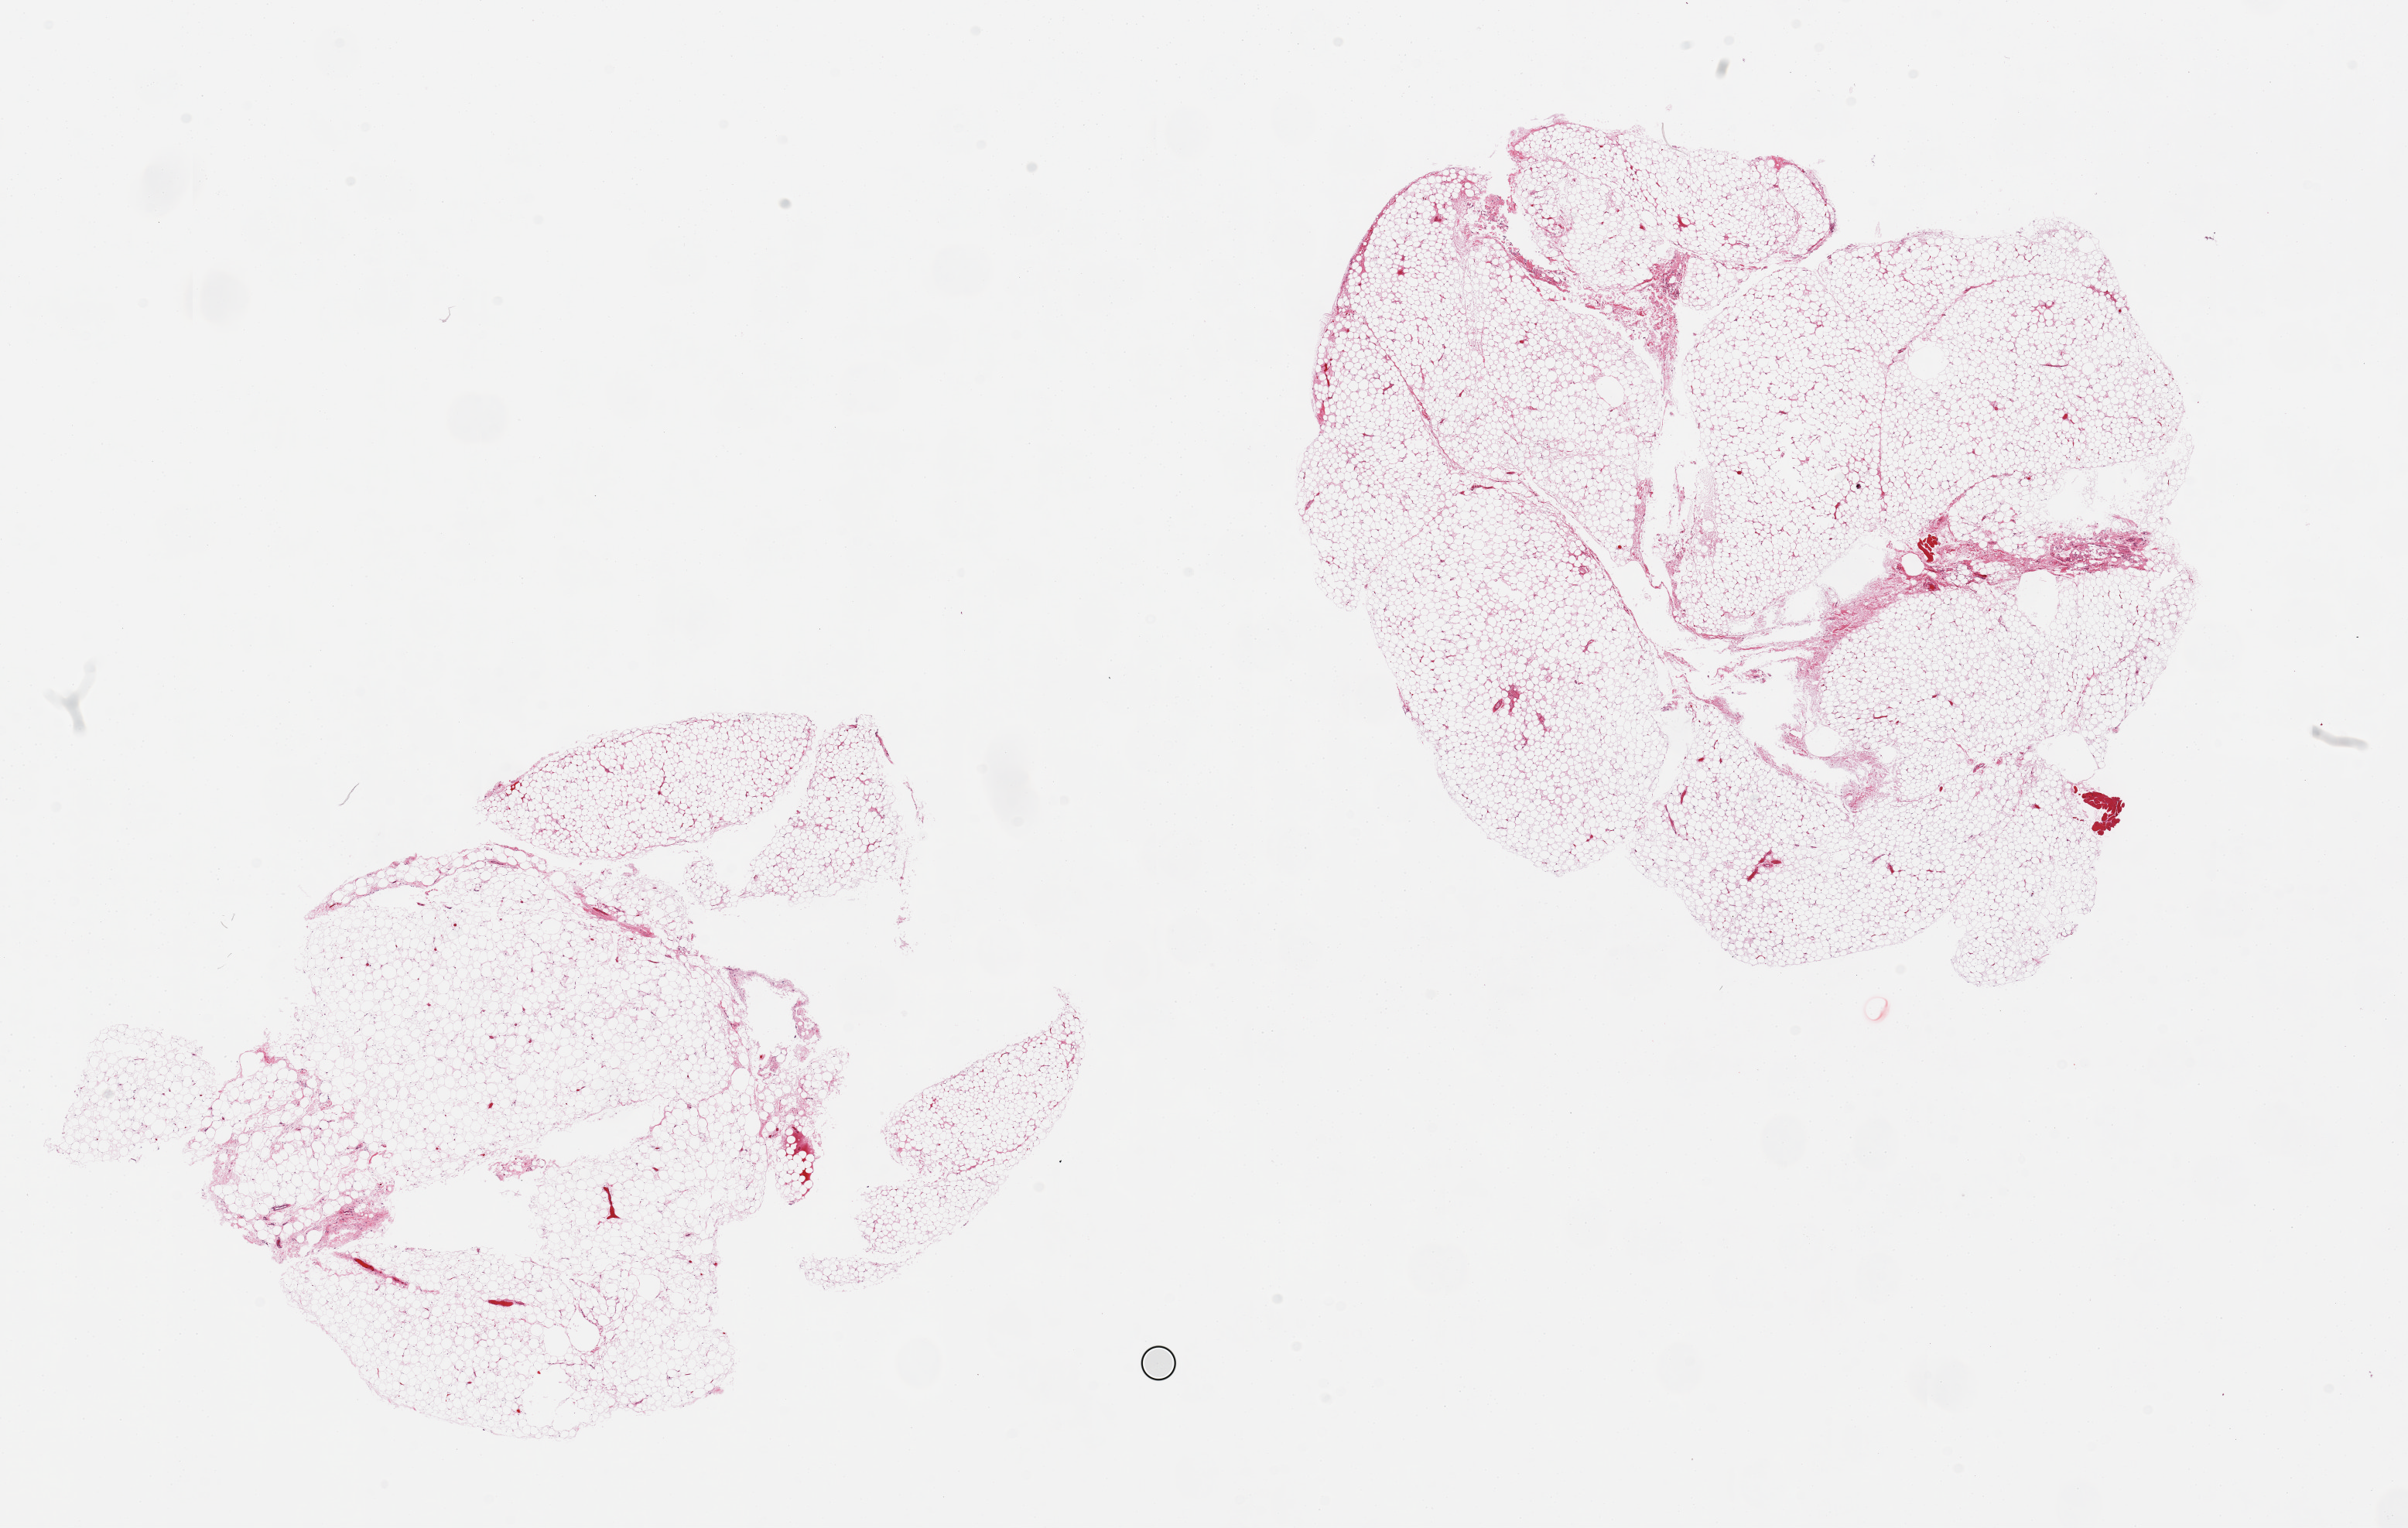
Digitized haematoxylin and eosin-stained section, a low-resolution overview of the entire scanned area, about 24.6 x 15.6 mm (slide scanned at 20x); PAXgene-fixed, paraffin-embedded tissue; sampled site (target tissue): adrenal gland; tissue donor sample.
Review note (as recorded): 2 pieces, adipose tissue, not adrenal, few foci of skeletal muscle.